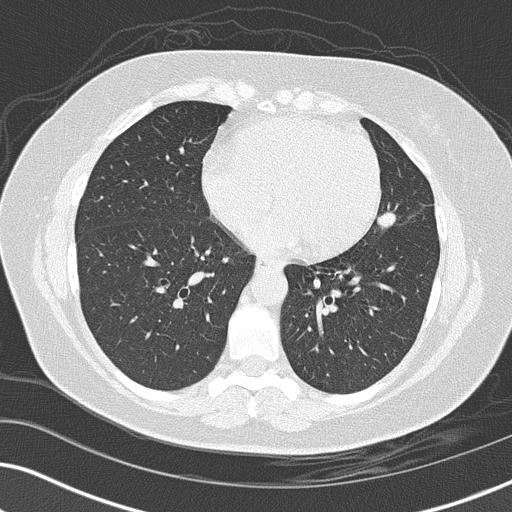
Chest CT (low-dose screening protocol), one axial image; third screening round (two years after baseline); lung window (W 1500 / L -600 HU); slice 87 of 152 in the series; 512 × 512 image matrix. Female participant, aged 56 years at enrolment. Former smoker at enrolment.
- Lesion marked by an expert reader, bounding box <357,198,410,245> (left, top, right, bottom; pixels).
- Reader record for this screening exam (exam-level; its link to the box is not recorded): non-calcified nodule or mass ≥4 mm, lingula, 14 × 14 mm, spiculated (stellate) margins, soft tissue attenuation, pre-existing on the prior screen: yes; interval growth: yes.
- Lung cancer was diagnosed 86 days after this screen: adenocarcinoma, NOS, left upper lobe, poorly differentiated (G3), stage IIIA (AJCC 6th edition), 15 mm at pathology.